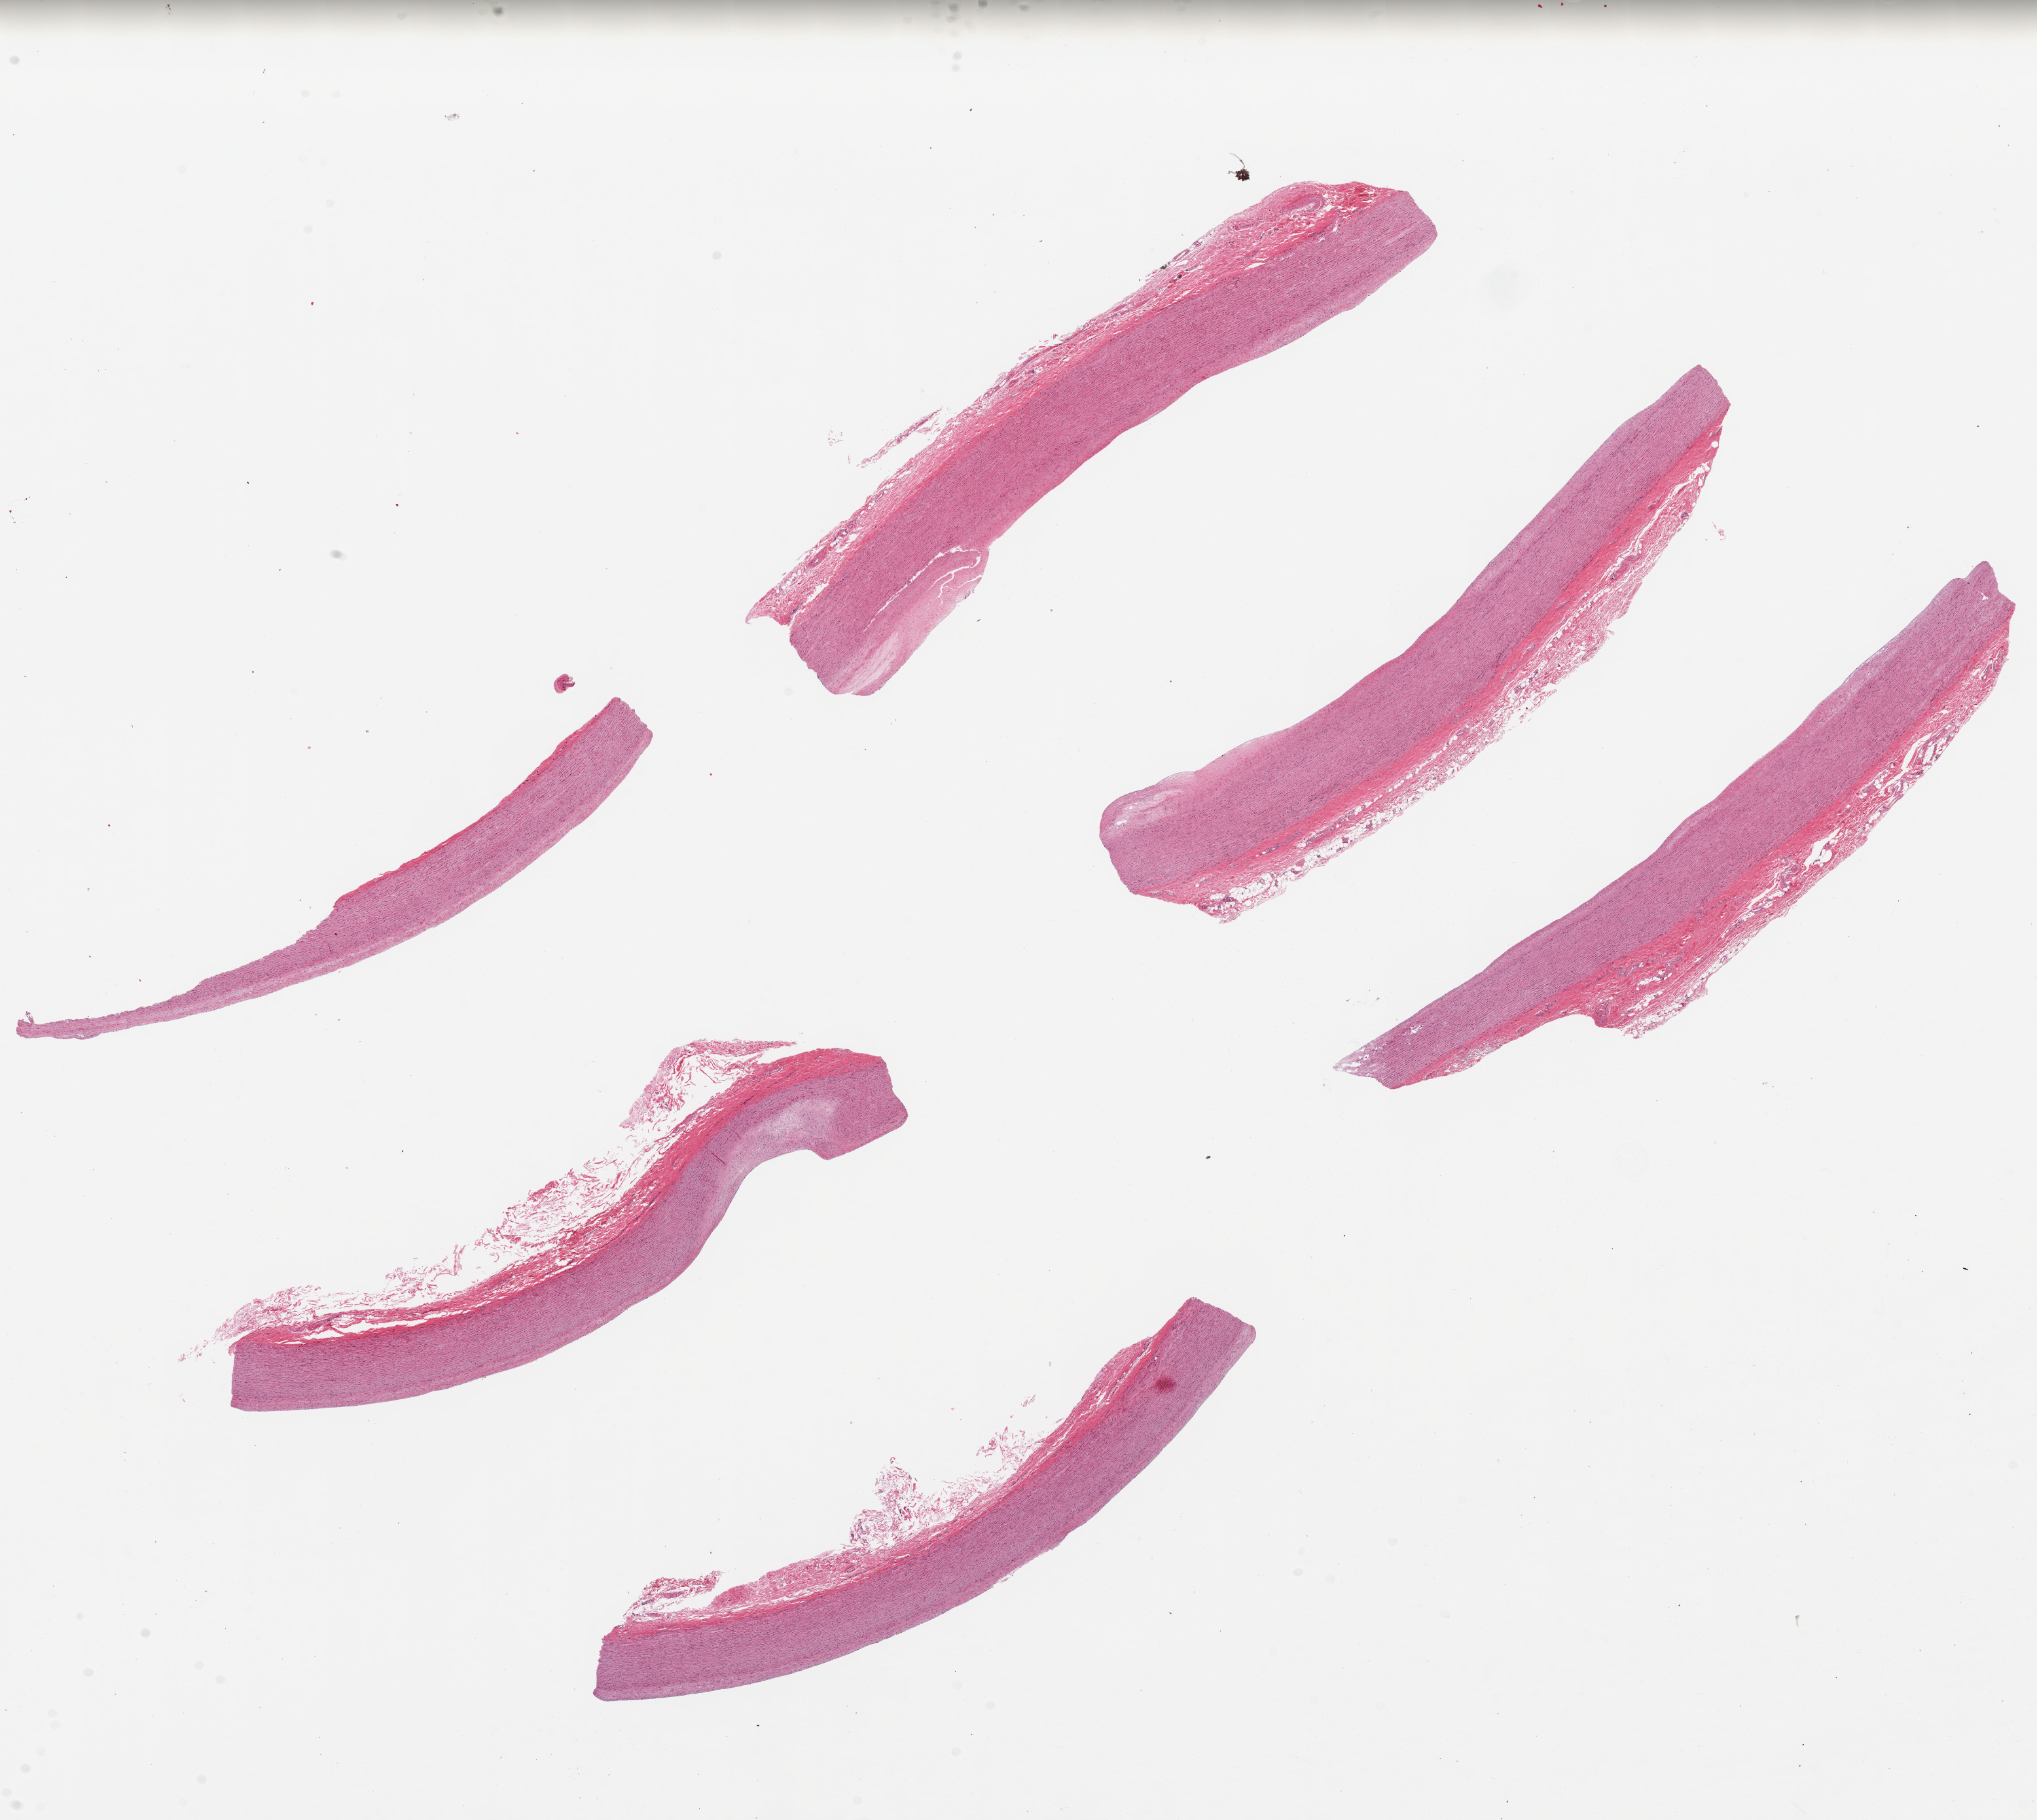
Whole-slide image, haematoxylin and eosin stain — low-resolution overview of the scanned area, about 24.6 x 22.0 mm (from a 20x scan). PAXgene-fixed, paraffin-embedded tissue. Target tissue: aorta. Tissue donor sample. Donor: female.
Pathologist's review note for this sample: 6 ~9x1.5mm pieces, patchy atheromatous deposition.